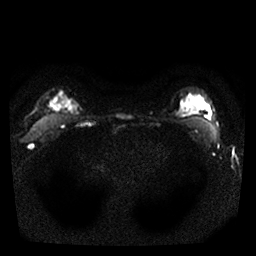
Breast MRI, one axial slice; slice 23 of 25 in the series (ordered by position); diffusion-weighted series; image 2 of 4 stored at this slice position (different b-values; order by instance number); 1.5 T; 4 mm slice thickness; 256 × 256 image matrix. Female patient.
Annotated regions visible in this slice (outlined manually by an expert reader):
- tumour on diffusion-weighted imaging: box from (x=50, y=98) to (x=80, y=115) px